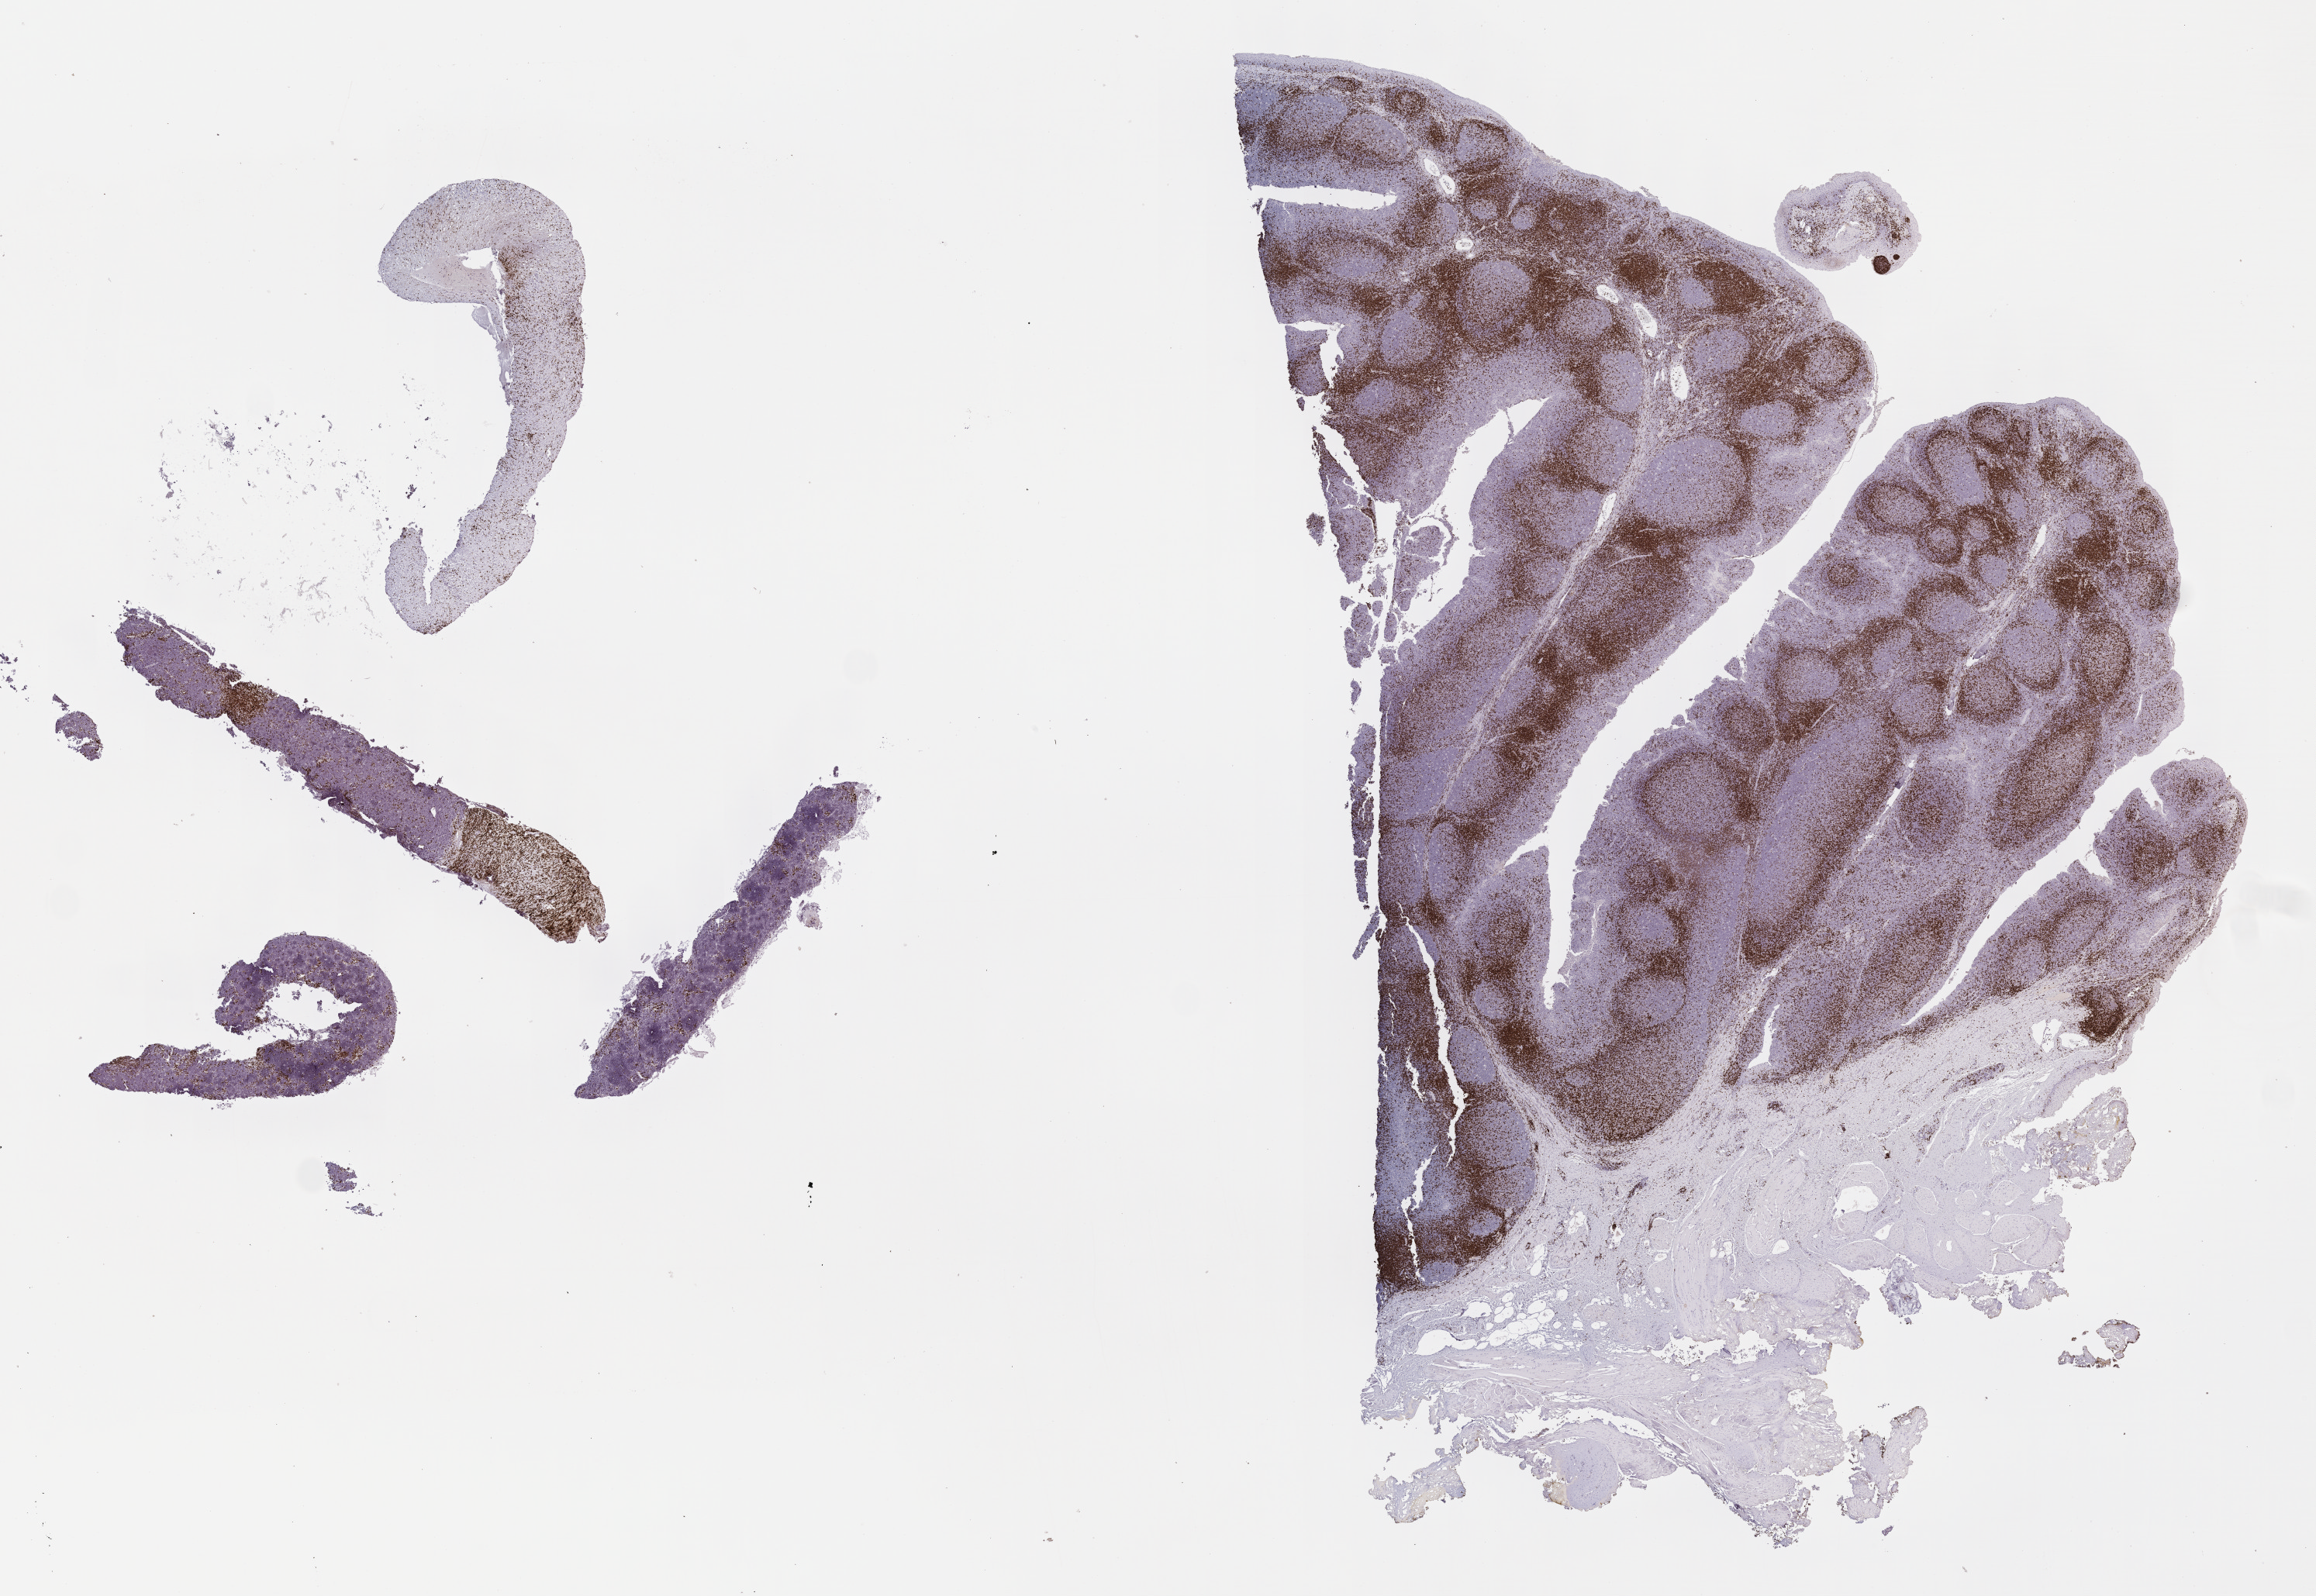
IHC for CD3, whole-slide image — shown as a low-resolution overview of the whole scanned area (about 24.2 x 16.6 mm). Patient sex: male.
- specimen: tumor tissue